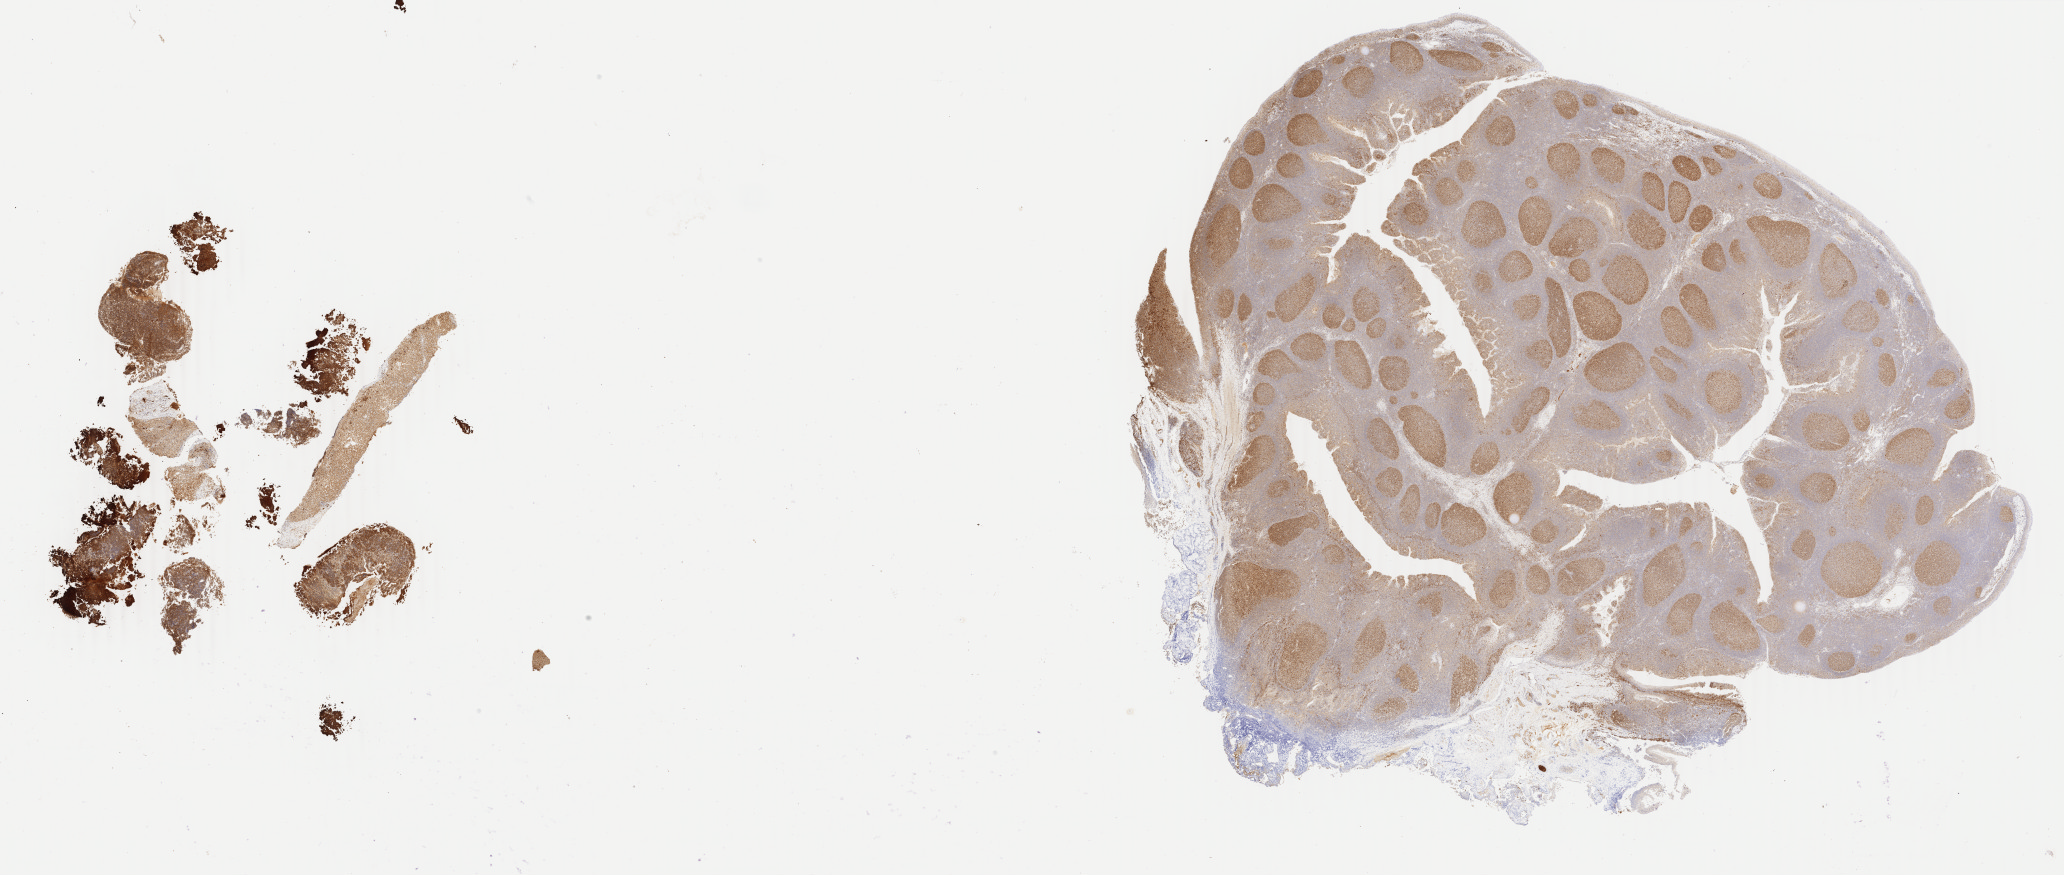
Immunohistochemistry (IHC) whole-slide image stained for BCL6, shown as a low-resolution overview of the whole scanned area (about 32.8 x 13.9 mm). Specimen: tumor tissue. Anatomic site: liver. Male, age 5 years at initial diagnosis.
Diagnosis: Burkitt lymphoma, NOS.